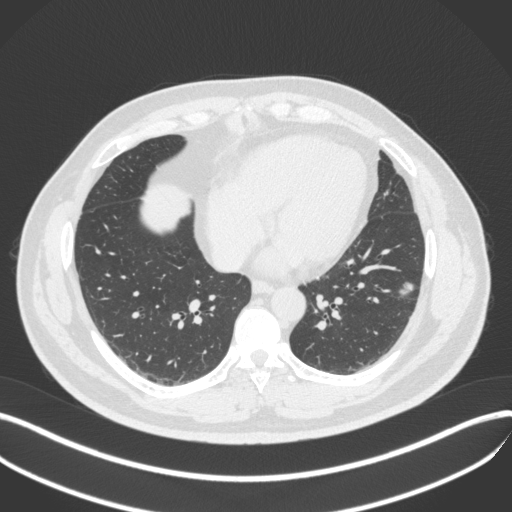
Chest CT, one axial slice; slice 154 of 420 in the series (ordered by position); lung window (W 1500 / L -600 HU); 512 × 512 image matrix. Male patient, age 39 years. Case-level facts recorded for this patient, not image findings: clinical TNM (as recorded): T2a N0 M0.
Structures marked on this image (rectangle marked by the reading radiologist):
- lung tumour (recorded histology: adenocarcinoma): bounding box [x1, y1, x2, y2] px = [394, 278, 415, 304]